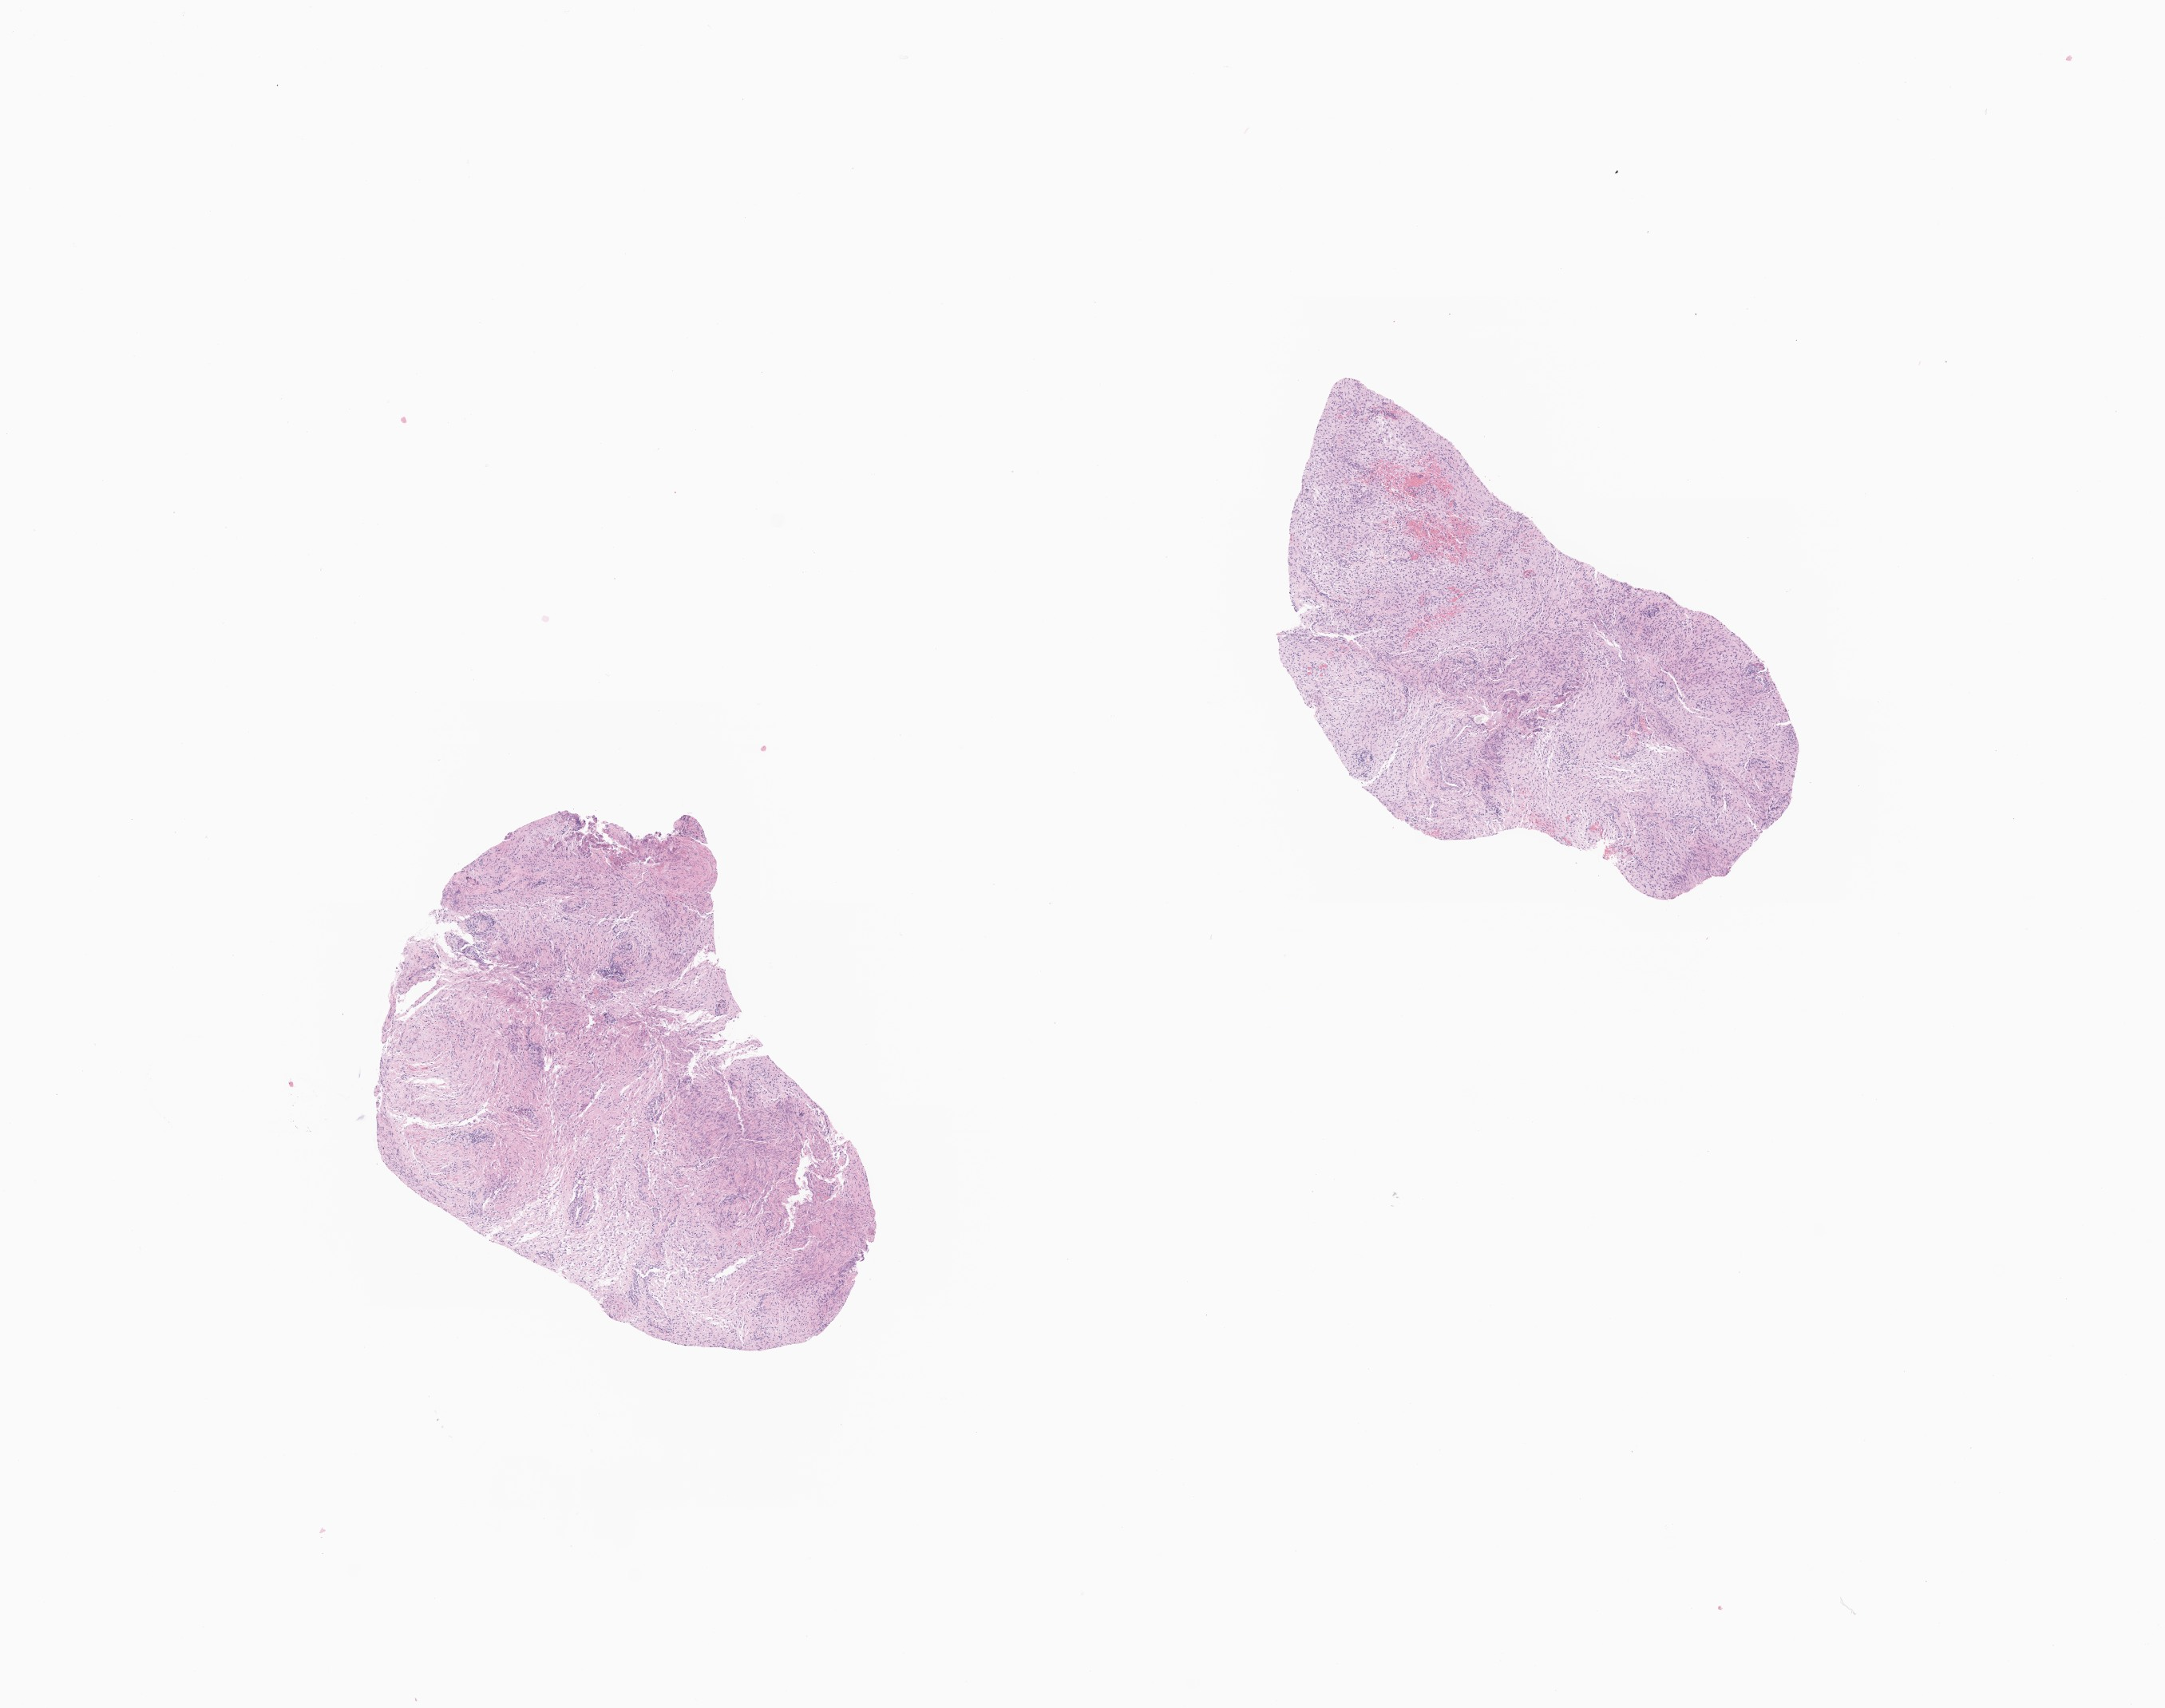
Hematoxylin and eosin (H&E) whole-slide image of tumor tissue from the brain, whole scanned area (about 11.4 x 9.0 mm) shown as a low-resolution overview, FFPE section. Patient male; age 92 months (7 years 8 months).
- recorded diagnosis: Glioma, malignant